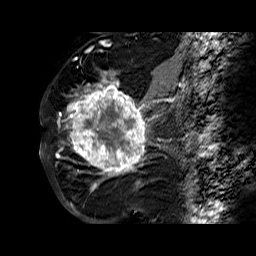
Breast MRI (dynamic contrast-enhanced), one sagittal slice. Slice 36 of 60 in the series (ordered by position). Dynamic contrast-enhanced series, time point 2 of 6 at this slice position (early post-contrast). 1.5 T. TE 6.3 ms, TR 32.4 ms. 4 mm slice thickness. 256 × 256 image matrix. Female patient. From the clinical record (not read from this slice): setting: breast cancer imaged before/during neoadjuvant chemotherapy; receptor status: HR-positive, HER2-negative.
Structures marked on this image (semi-automatically segmented with operator editing):
- analysis volume of interest (the breast-tissue region the enhancement analysis was run in; not a lesion): bounding box <68,72,177,183> (left, top, right, bottom; pixels)
- tumour enhancement mask (voxels above the 100 % enhancement threshold inside the analysis volume of interest): <68,72,170,179>